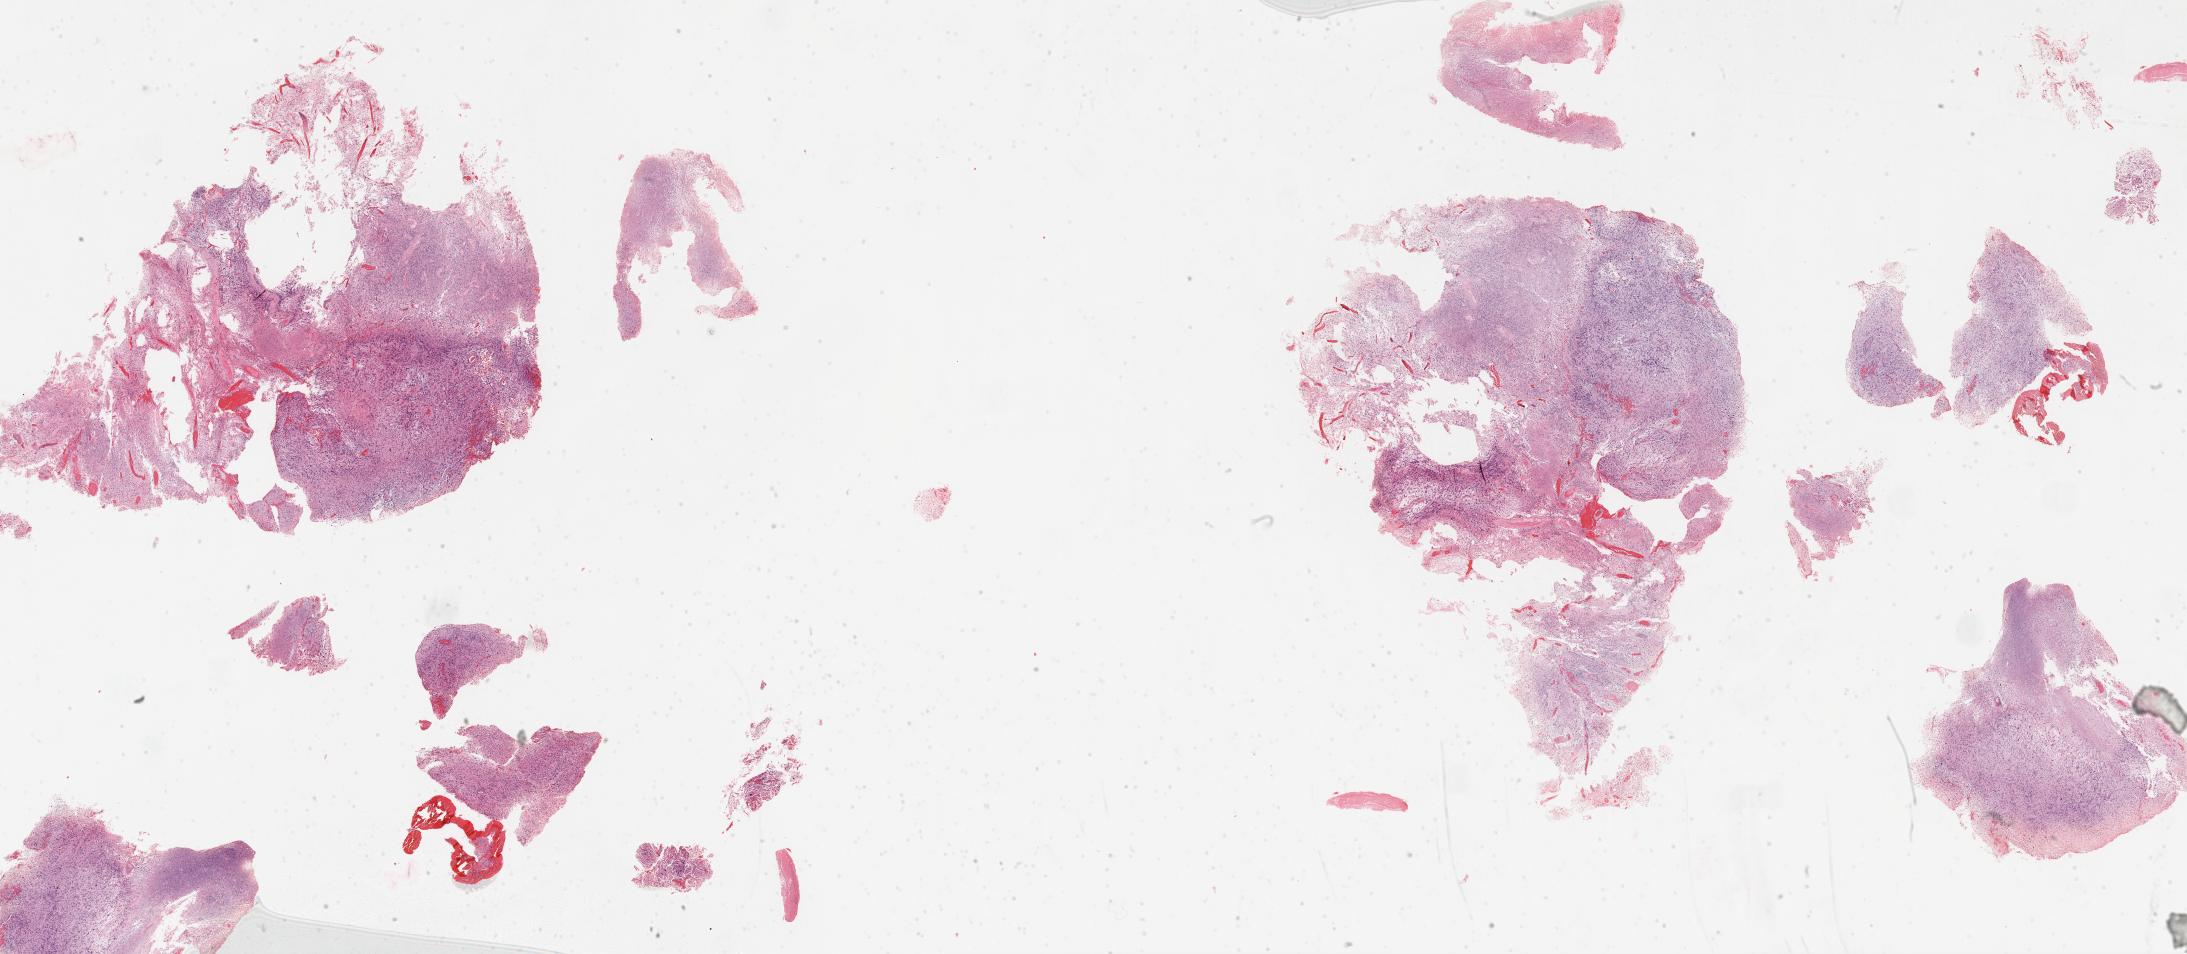
Digitized Hematoxylin and eosin (H&E) stained tissue section (whole slide), whole scanned area (about 35.1 x 15.3 mm) shown as a low-resolution overview. Formalin-fixed paraffin-embedded (FFPE) diagnostic section. Brain, primary tumour sample. Patient: female, age at initial diagnosis 60 years.
Histologic diagnosis: Glioblastoma.